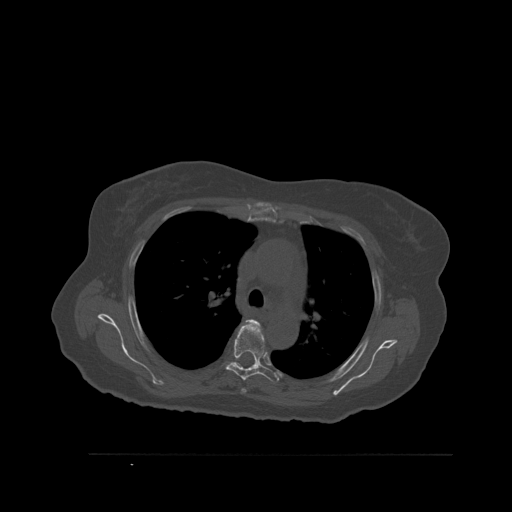
CT including the spine, one axial slice. Position 396 of 527 along the scan axis. Bone window (W 1800 / L 400 HU). 512 × 512 image matrix, field of view 470 × 470 mm. Patient: female, 73 years. From the clinical record (not read from this slice): primary cancer: breast; vertebrae with lytic lesions (as recorded): L2.
Outlined on this slice (semi-automatic segmentation, software-assisted and operator-edited):
- T4 vertebra: bounding box (x1, y1, x2, y2) in pixels: (241, 319, 264, 393)
- T5 vertebra: (223, 326, 280, 383)